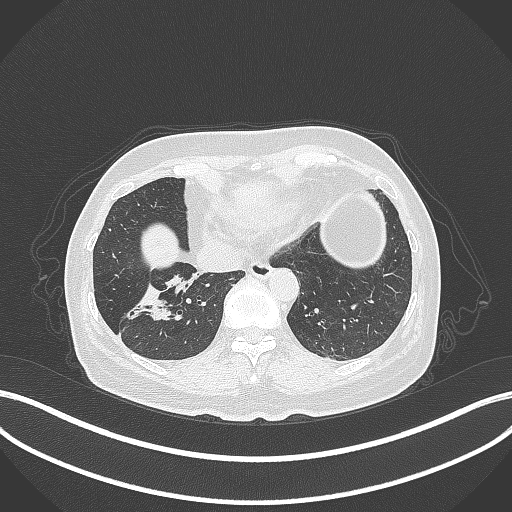
Chest CT, one axial slice. Position 107 of 429 along the scan axis. Reconstruction kernel B70f. Lung window (W 1500 / L -600 HU). 1 mm slice thickness. 512 × 512 image matrix. Female patient, age 67 years. From the clinical record (not read from this slice): clinical TNM (as recorded): T1c N1 M0; histopathological grade: G2-3.
Structures marked on this image (rectangle marked by the reading radiologist):
- lung tumour (recorded histology: adenocarcinoma): bounding box [x1, y1, x2, y2] px = [126, 275, 198, 330]